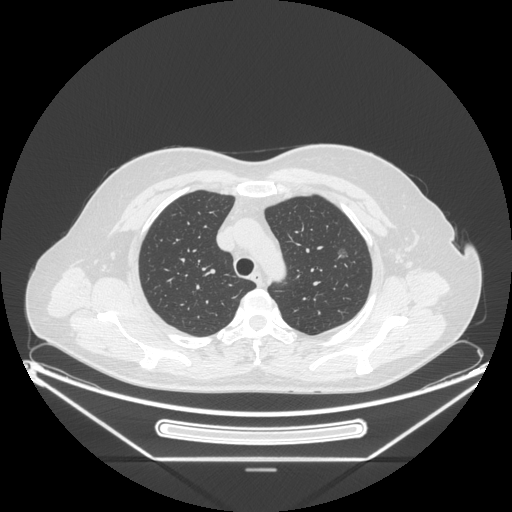
Chest CT, one axial slice; position 169 of 226 along the scan axis; reconstruction kernel STANDARD; 120 kVp; lung window (W 1500 / L -600 HU); 1.25 mm slice thickness; 512 × 512 image matrix, field of view 447 × 447 mm. Patient: female, 54 years. Case-level facts recorded for this patient, not image findings: clinical TNM (as recorded): T1c N0 M0.
Structures marked on this image (rectangle marked by the reading radiologist):
- lung tumour (recorded histology: adenocarcinoma): bounding box [x1, y1, x2, y2] px = [334, 245, 350, 270]